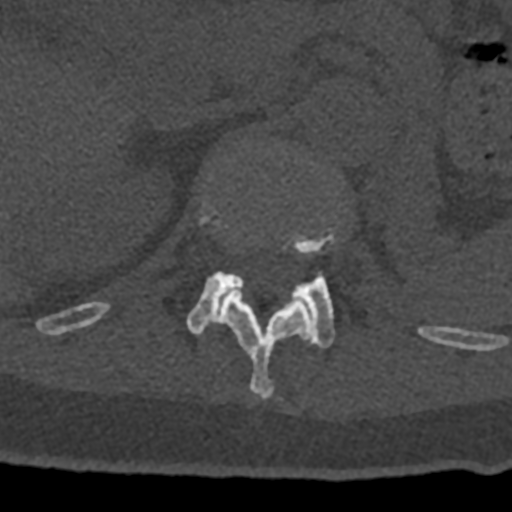
CT including the spine, one axial slice. Reconstruction kernel Br40s/3. 120 kVp. Bone window (W 1800 / L 400 HU). 0.5 mm slice thickness. 512 × 512 image matrix, field of view 160 × 160 mm. Patient: male, 74 years. From the clinical record (not read from this slice): primary cancer: renal.
Annotated regions visible in this slice (semi-automatically segmented with operator editing):
- L1 vertebra: box from (x=187, y=228) to (x=335, y=348) px
- T12 vertebra: (x=70, y=199)–(x=432, y=400)